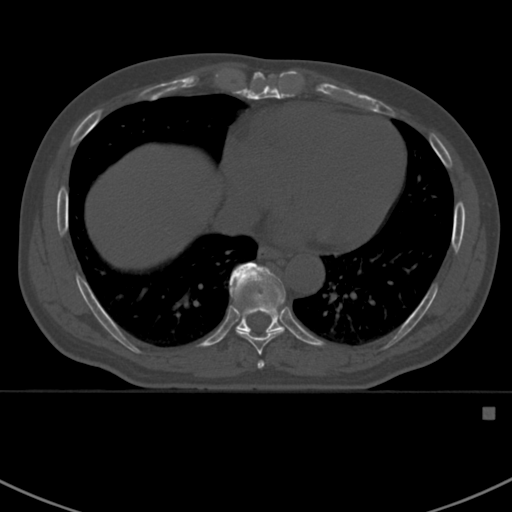
CT including the spine, one axial slice. Position 393 of 412 along the scan axis. Reconstruction kernel Br40s. 120 kVp. Bone window (W 1800 / L 400 HU). 1.5 mm slice thickness. 512 × 512 image matrix, field of view 358 × 358 mm. Male patient, age 59 years. Case-level facts recorded for this patient, not image findings: primary cancer: prostate.
Annotated regions visible in this slice (semi-automatic segmentation, software-assisted and operator-edited):
- T7 vertebra: bounding box <257,360,265,368> (left, top, right, bottom; pixels)
- T8 vertebra: <237,330,284,355>
- T9 vertebra: <230,262,285,333>